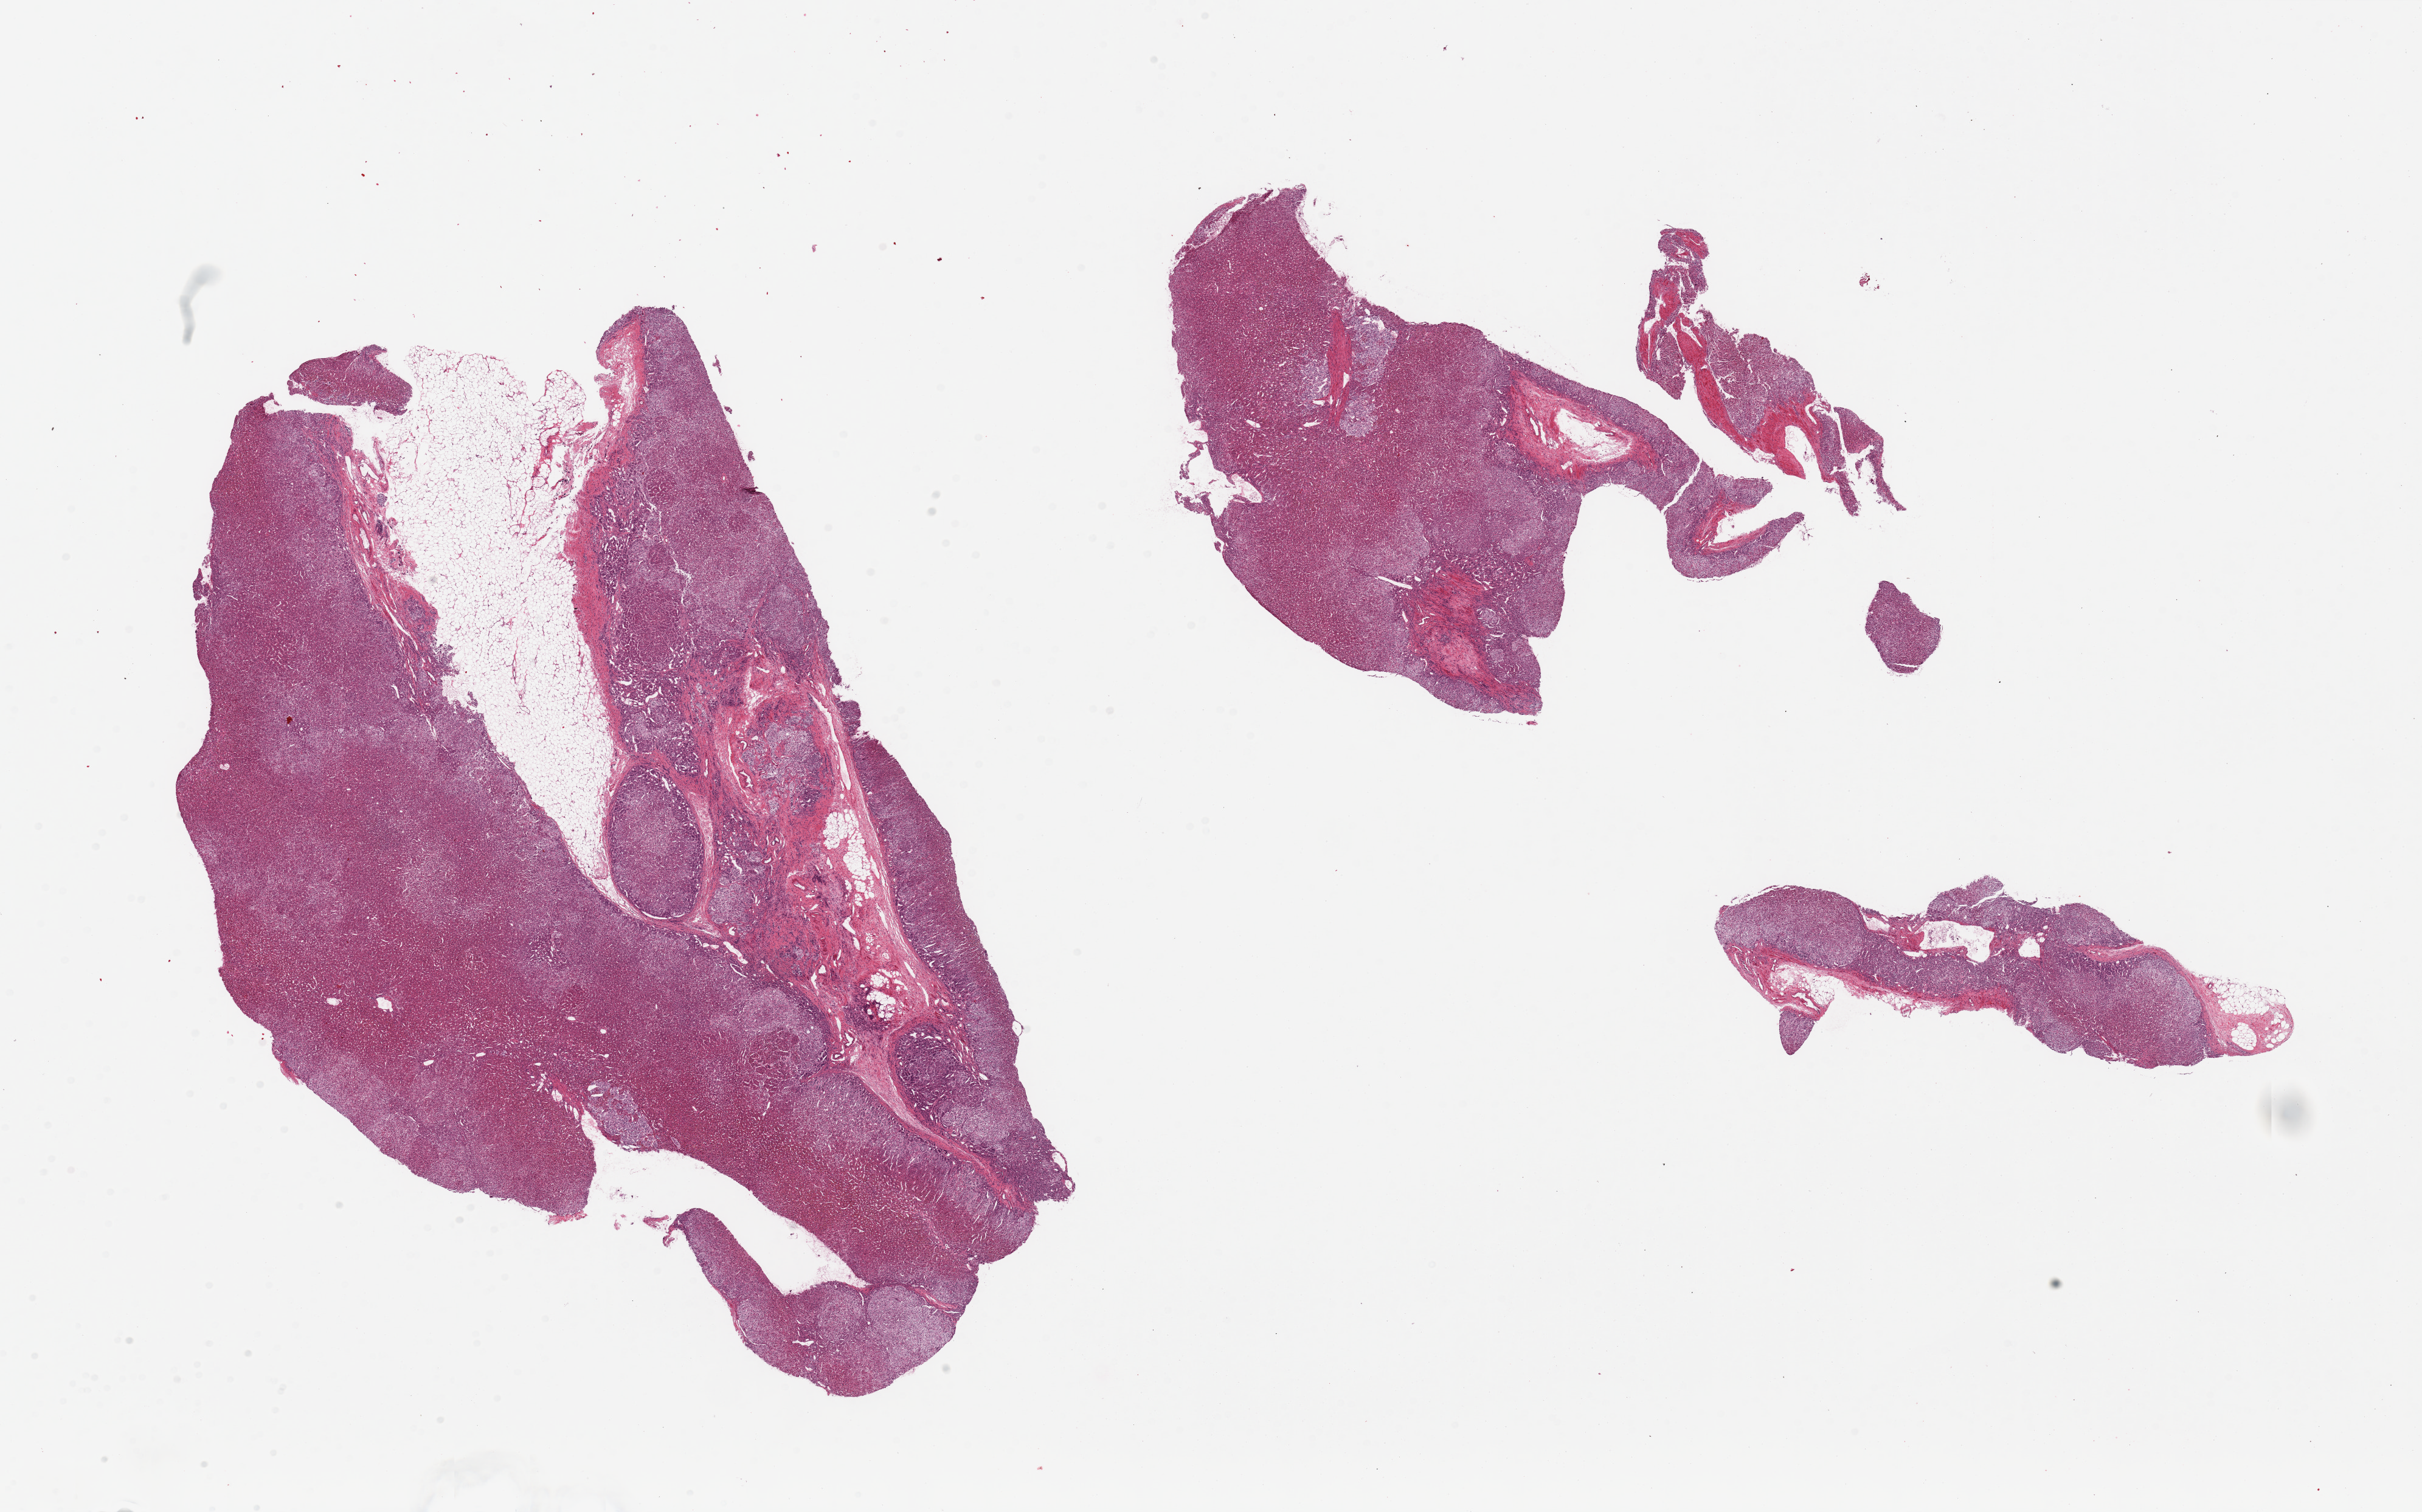
Whole-slide image, H&E stain — whole scanned area (about 31.5 x 19.7 mm, slide scanned at 20x) shown as a low-resolution overview. PAXgene-fixed, paraffin-embedded tissue. Sampled site (target tissue): adrenal gland. Tissue donor sample.
Reviewer comment on this tissue sample: 3 pieces, largest has 20% internal fat.